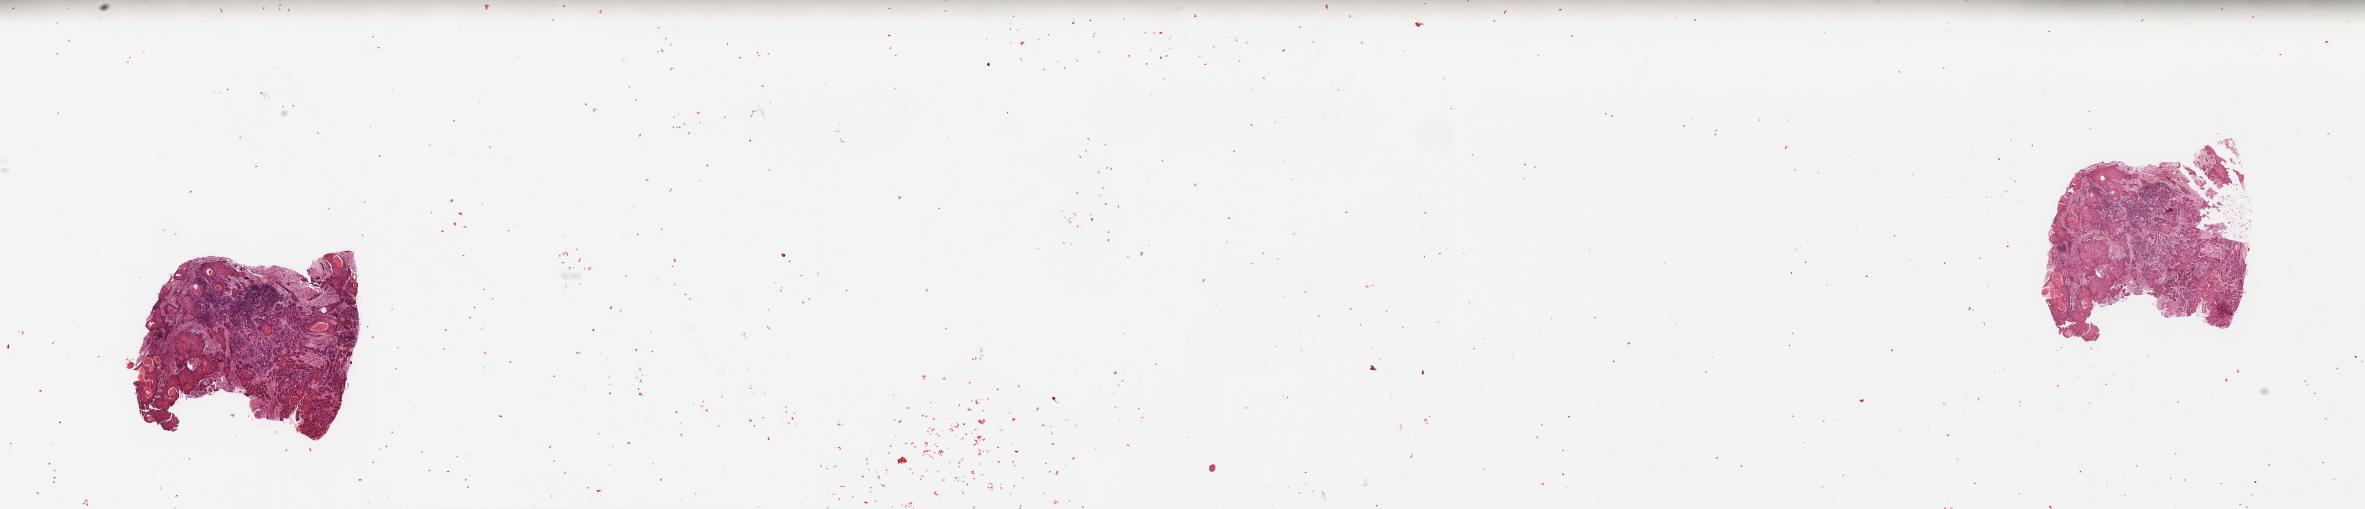
Digitized H&E-stained tissue section (whole slide) — a low-resolution overview of the entire scanned area, about 37.4 x 8.1 mm (from a 20x scan); head and neck, tissue type not recorded. 59-year-old male patient.
• patient diagnosis: Squamous cell carcinoma, NOS (floor of mouth, NOS)